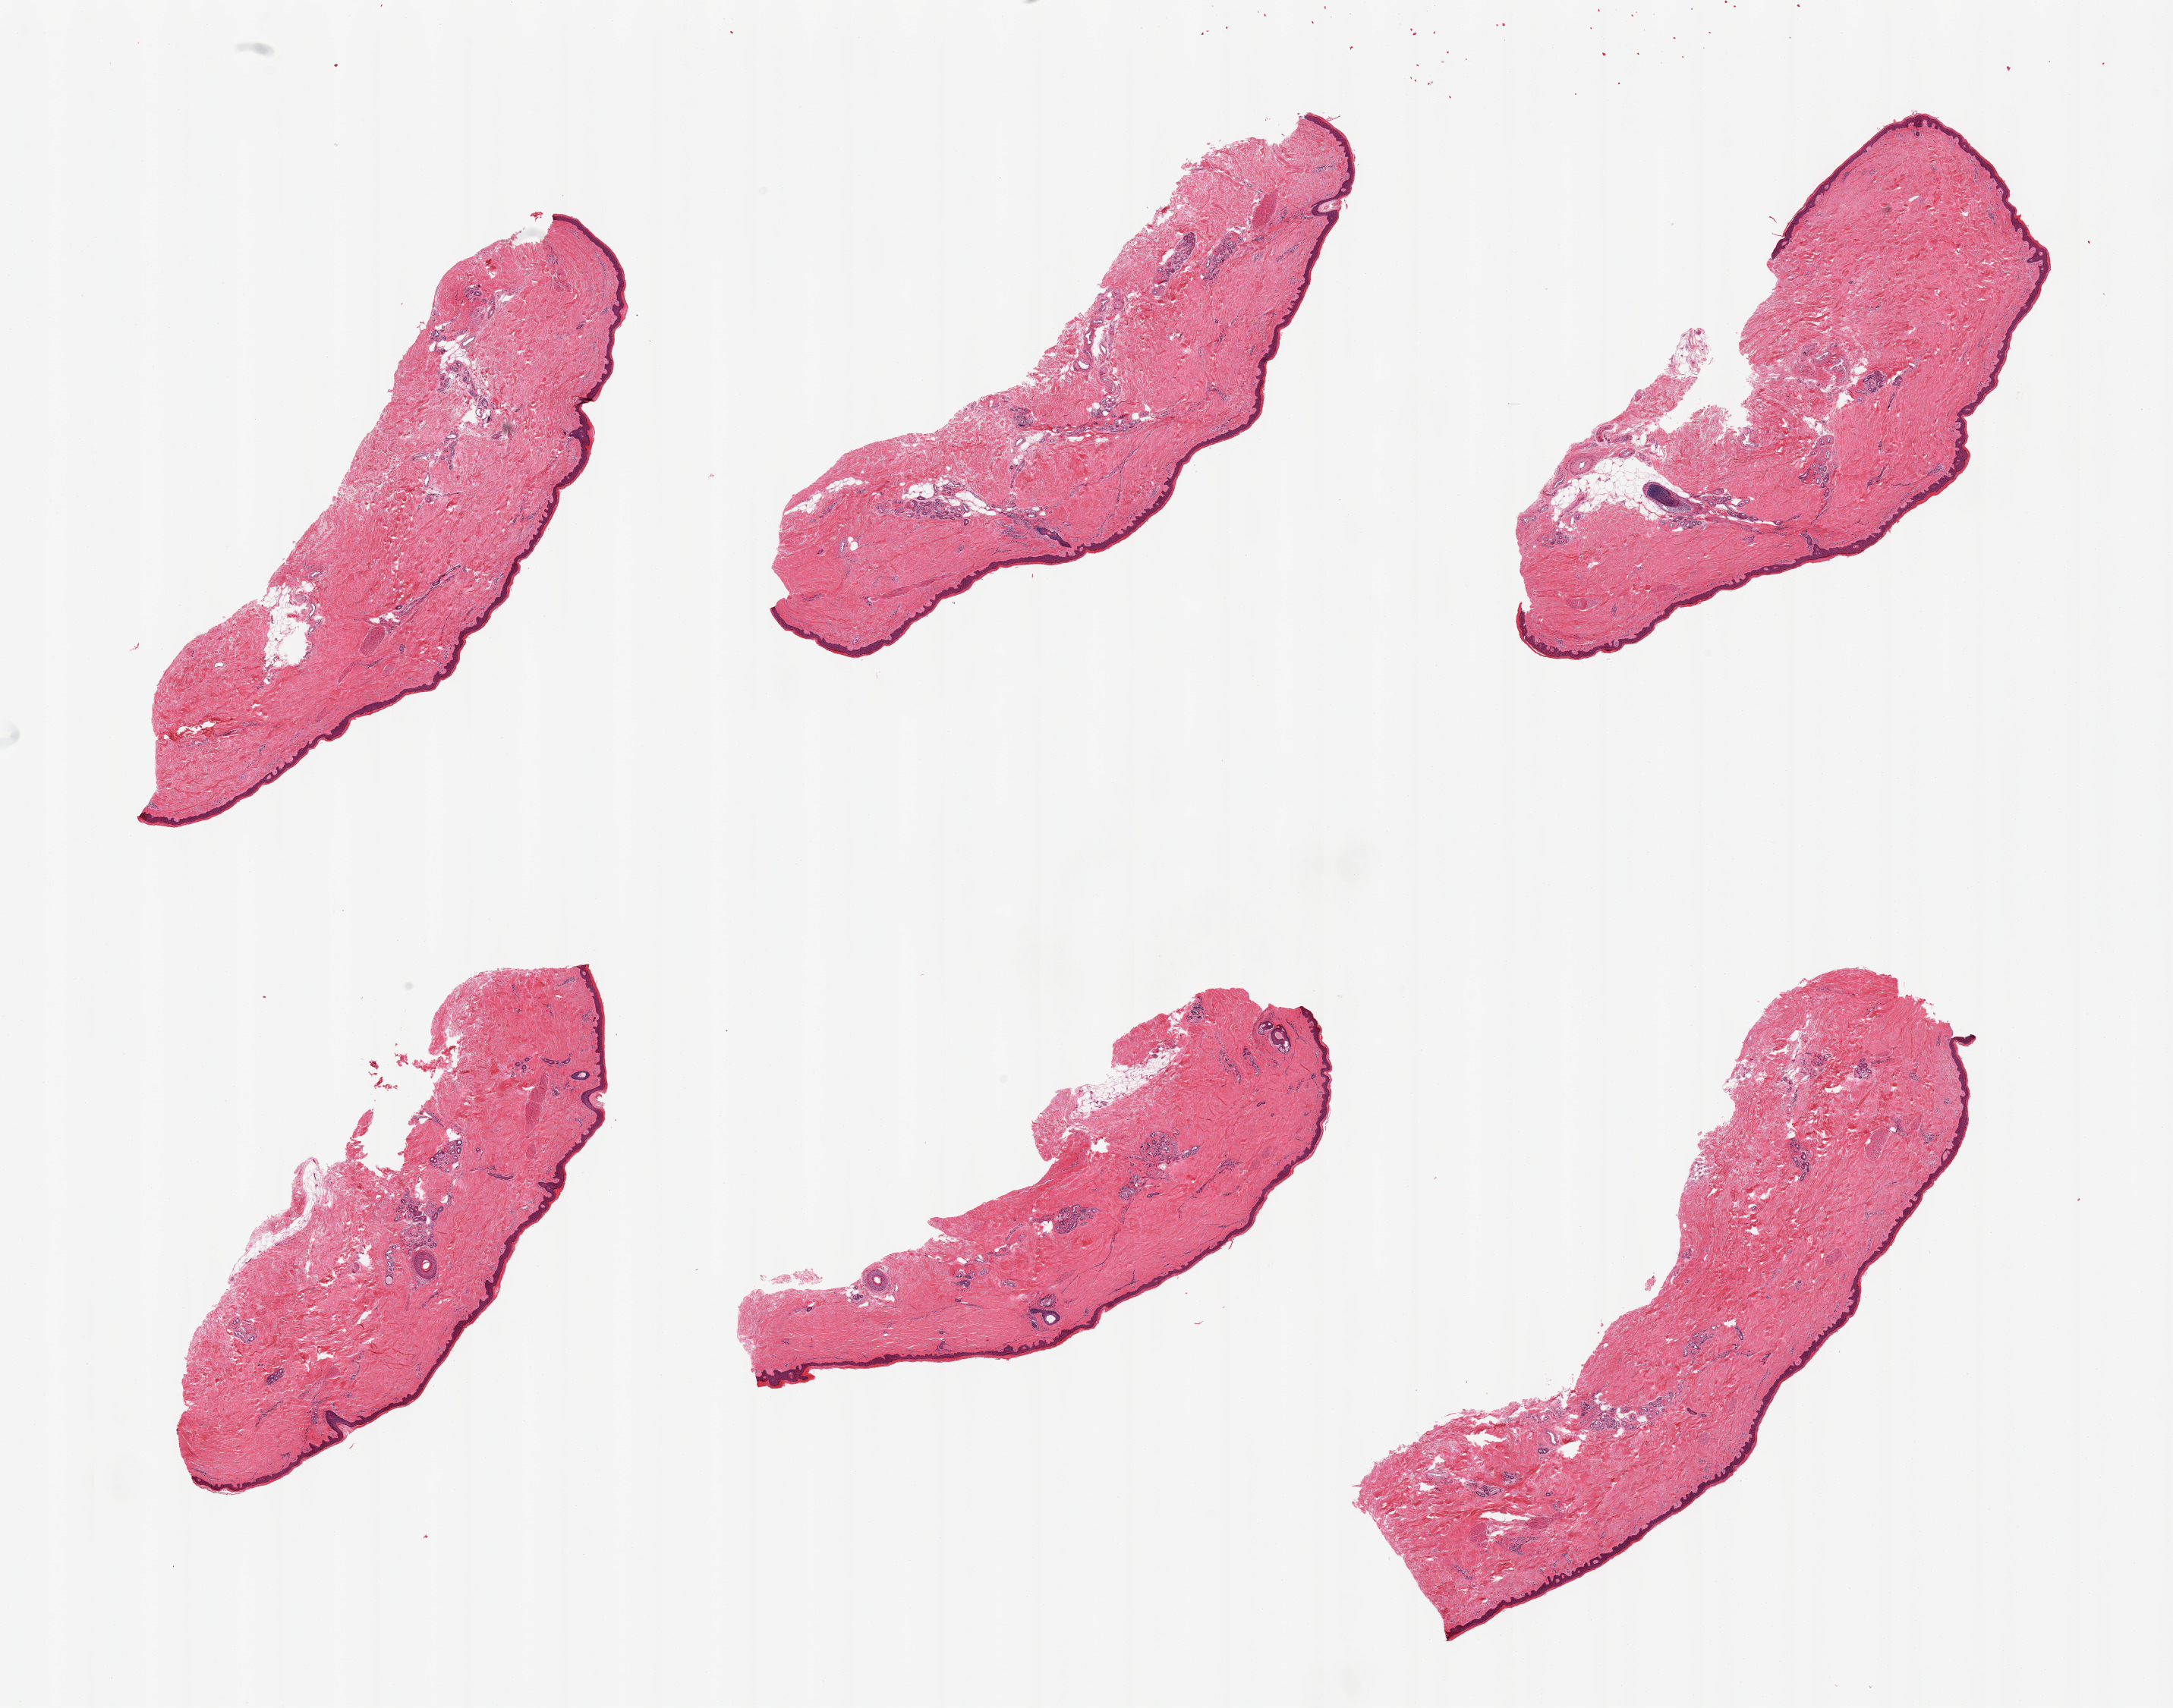
Whole-slide image, hematoxylin and eosin (H&E) stain — a low-resolution overview of the entire scanned area, about 22.6 x 17.8 mm; PAXgene-fixed, paraffin-embedded tissue; section of skin of lower leg (target tissue); tissue donor sample. Donor sex: male.
Review note (as recorded): 6 pieces, no dermal fat; squamous epithelium is ~50-60 microns.